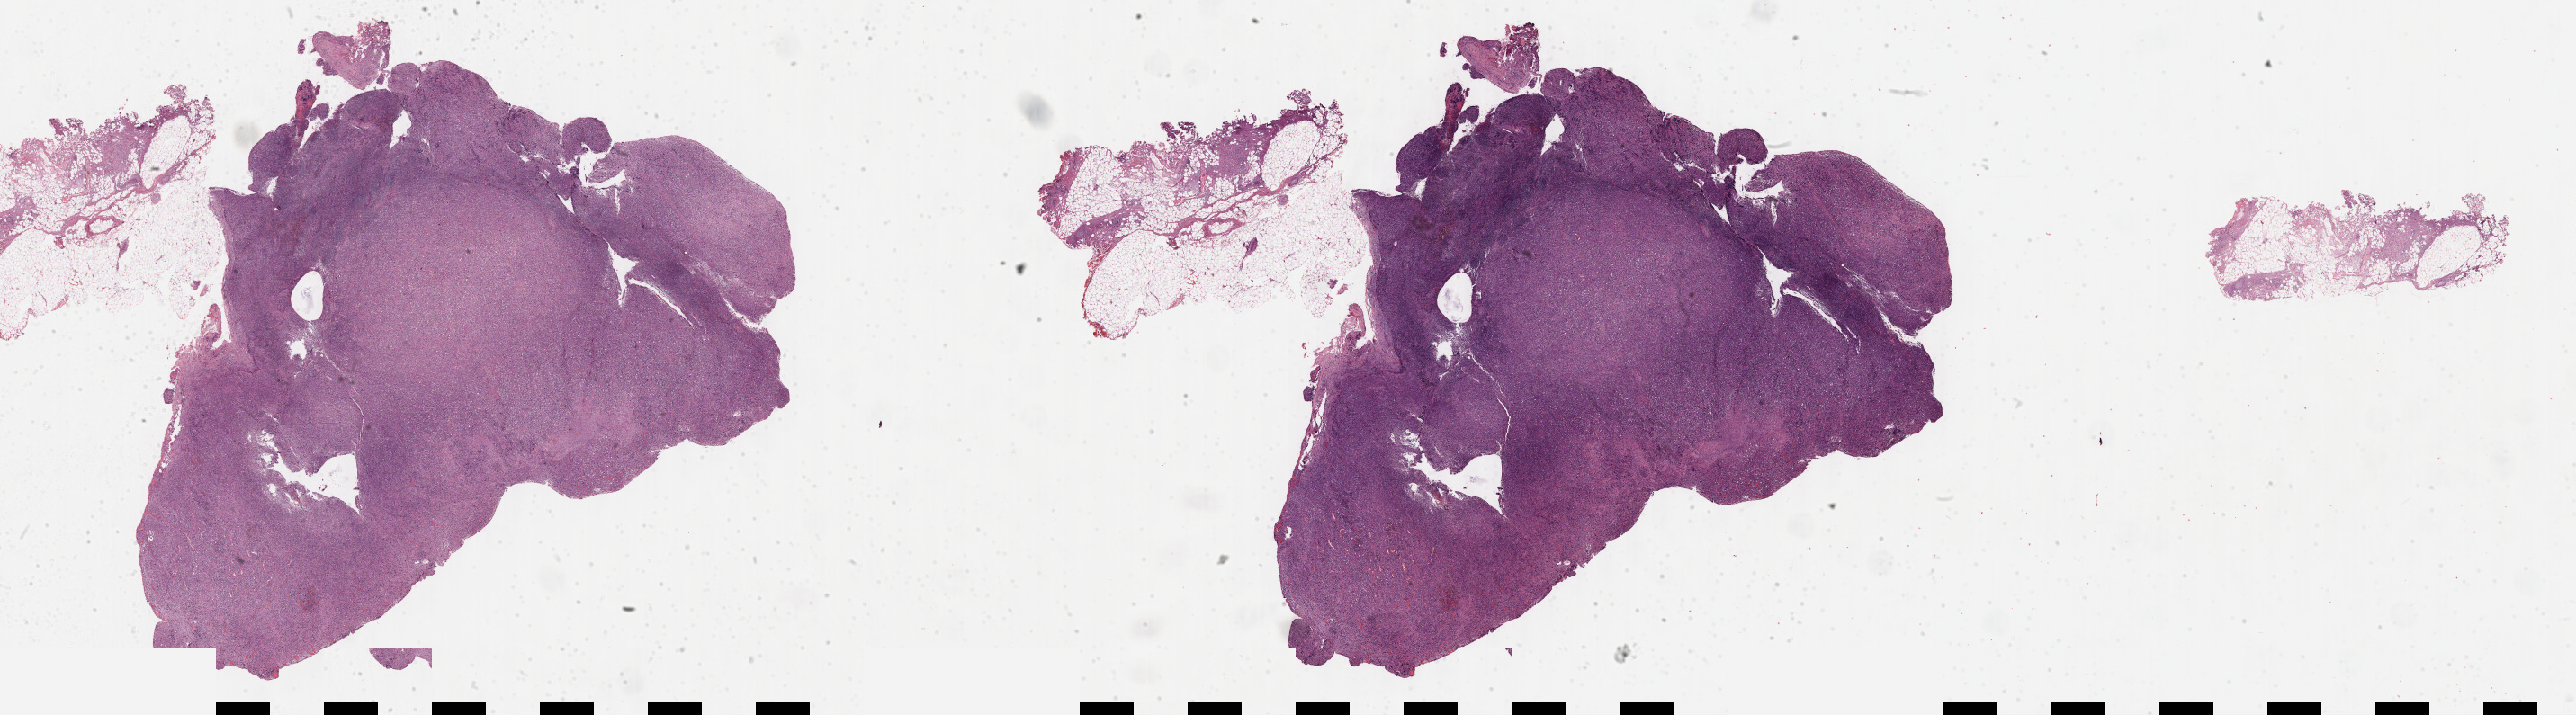
Whole-slide histology image, H&E-stained — a low-resolution overview of the entire scanned area, about 46.3 x 12.9 mm (acquisition: 40x scan), formalin-fixed paraffin-embedded (FFPE) diagnostic section, lymphoid tissue, primary tumour sample. Female patient; age at initial diagnosis 23 years.
Histologic diagnosis: Mediastinal (thymic) large B-cell lymphoma (lymph nodes of axilla or arm).